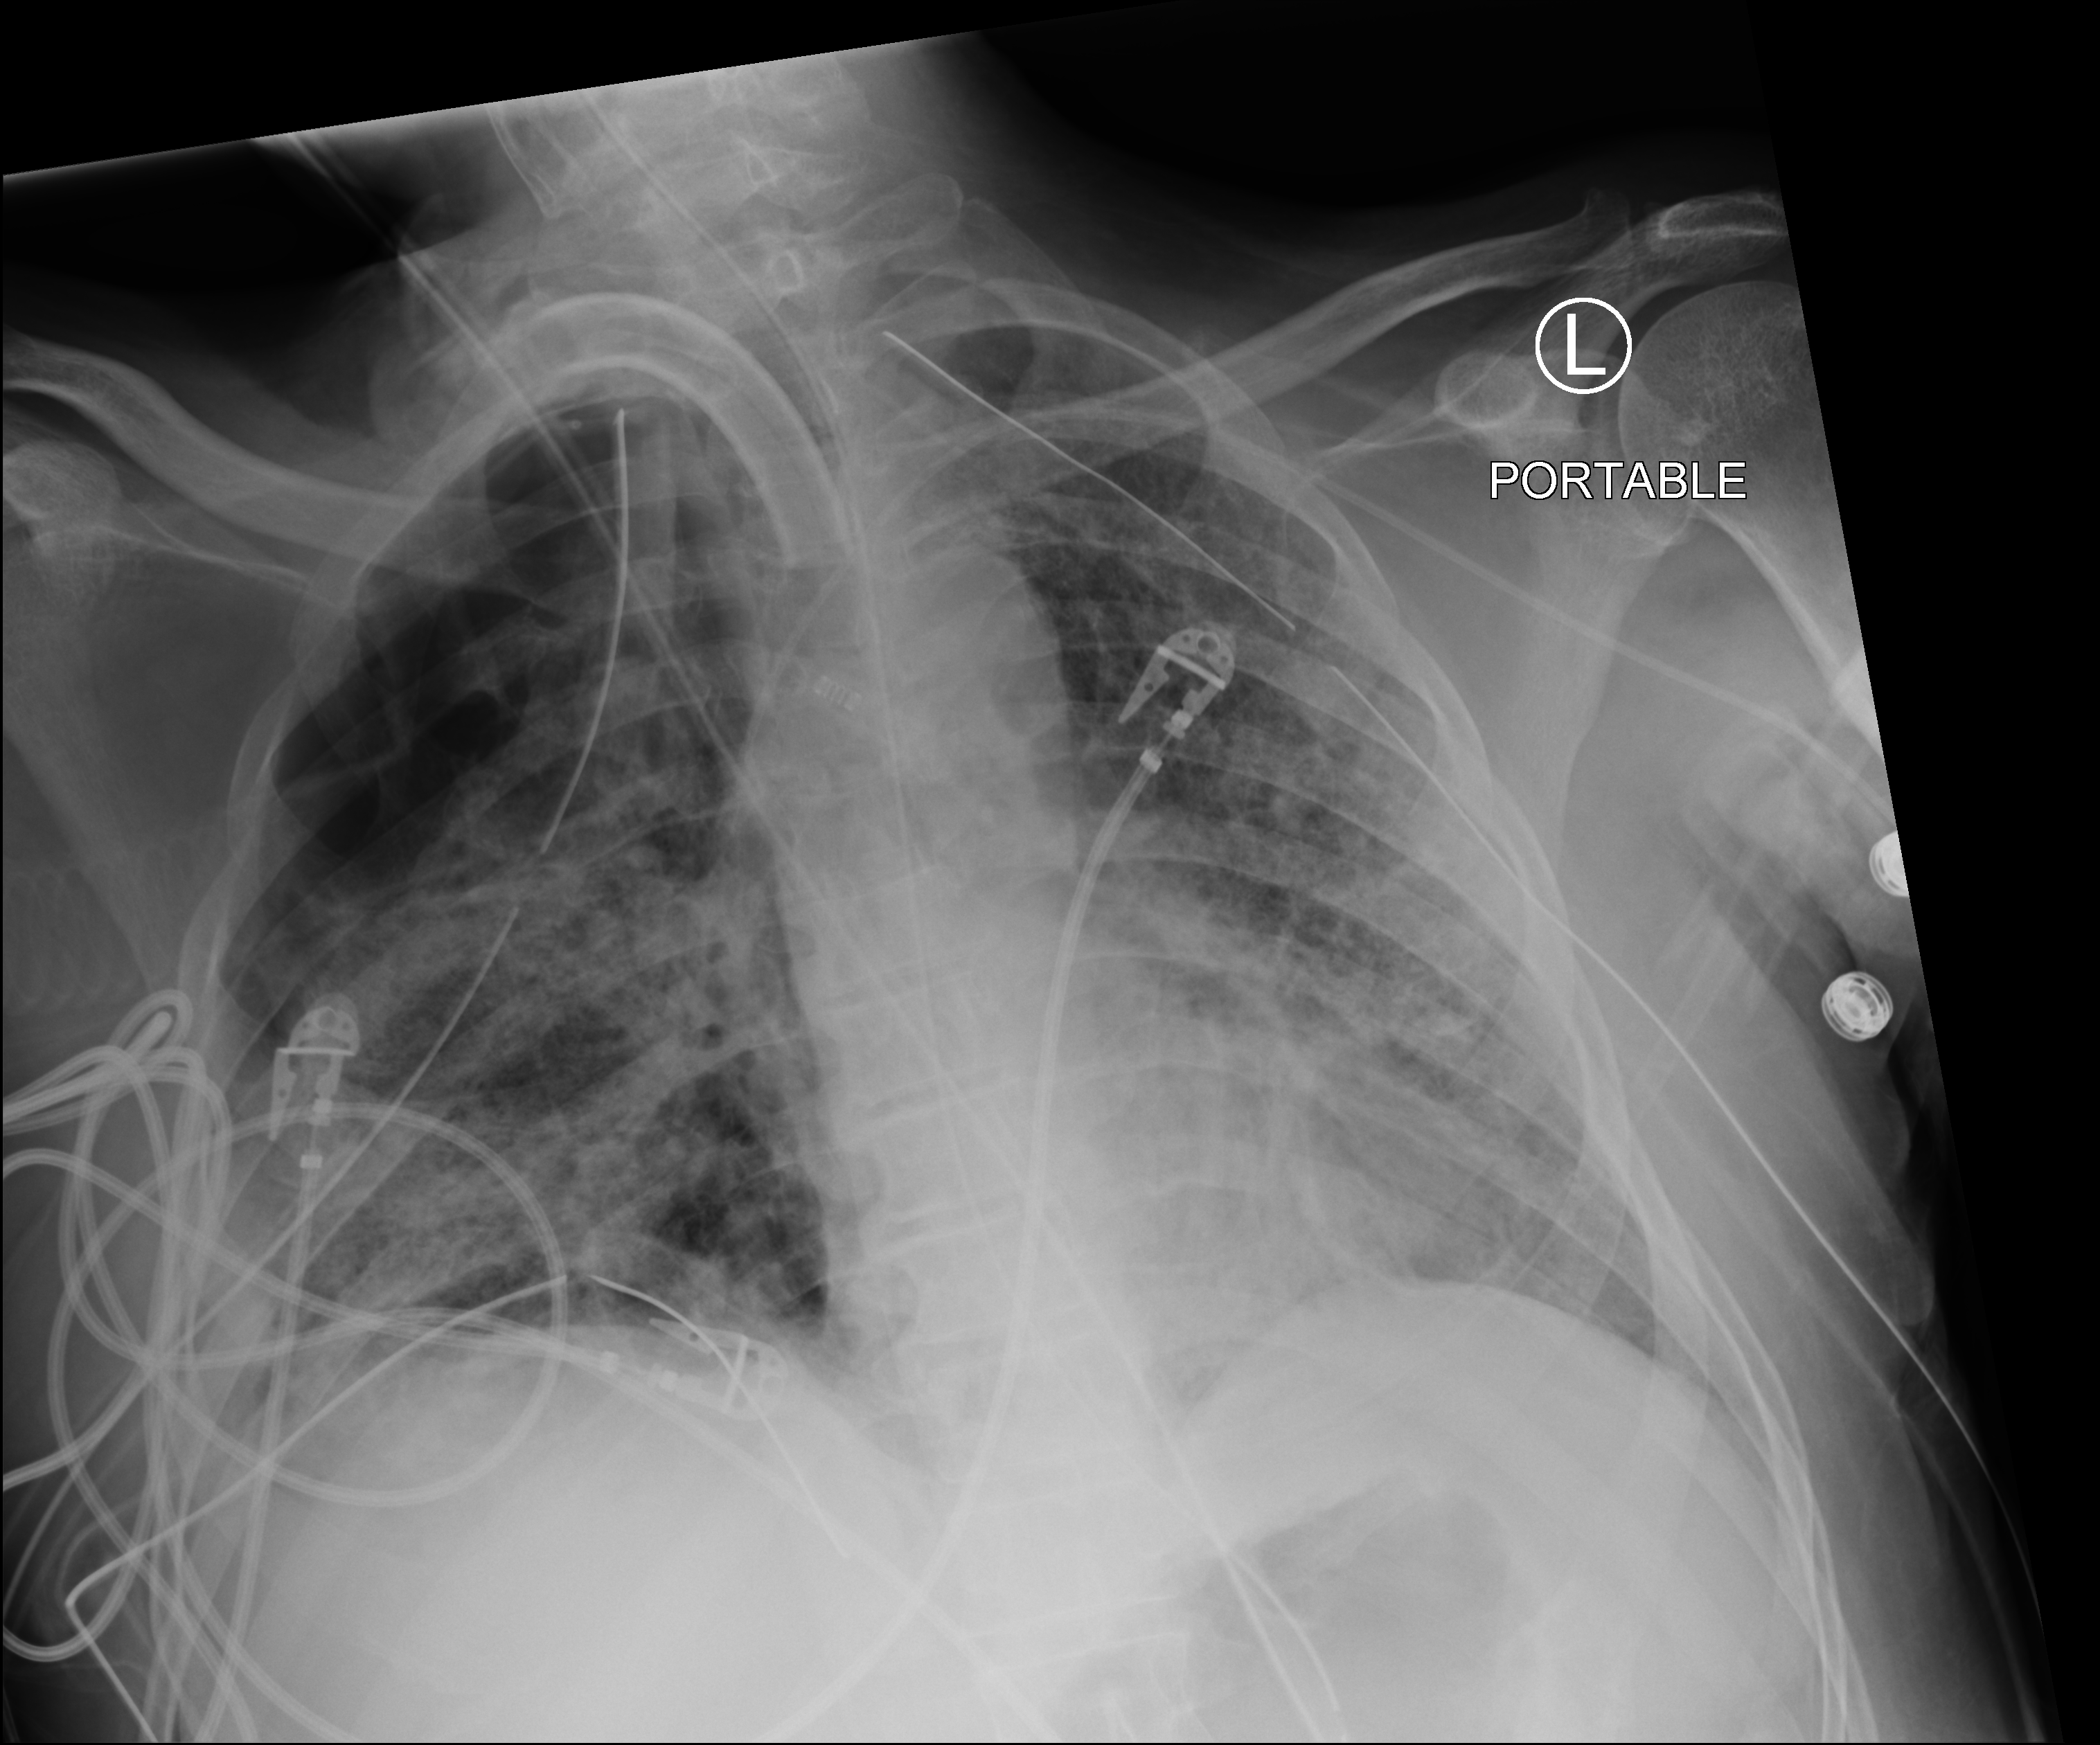
Bedside chest radiograph (computed radiography); anteroposterior (AP) projection. Patient hospitalised with COVID-19; male, aged 18–59 years.
From the hospital-stay record, not from the radiograph (when in the stay this image was taken is not recorded): admitted to intensive care during this hospital stay: yes.